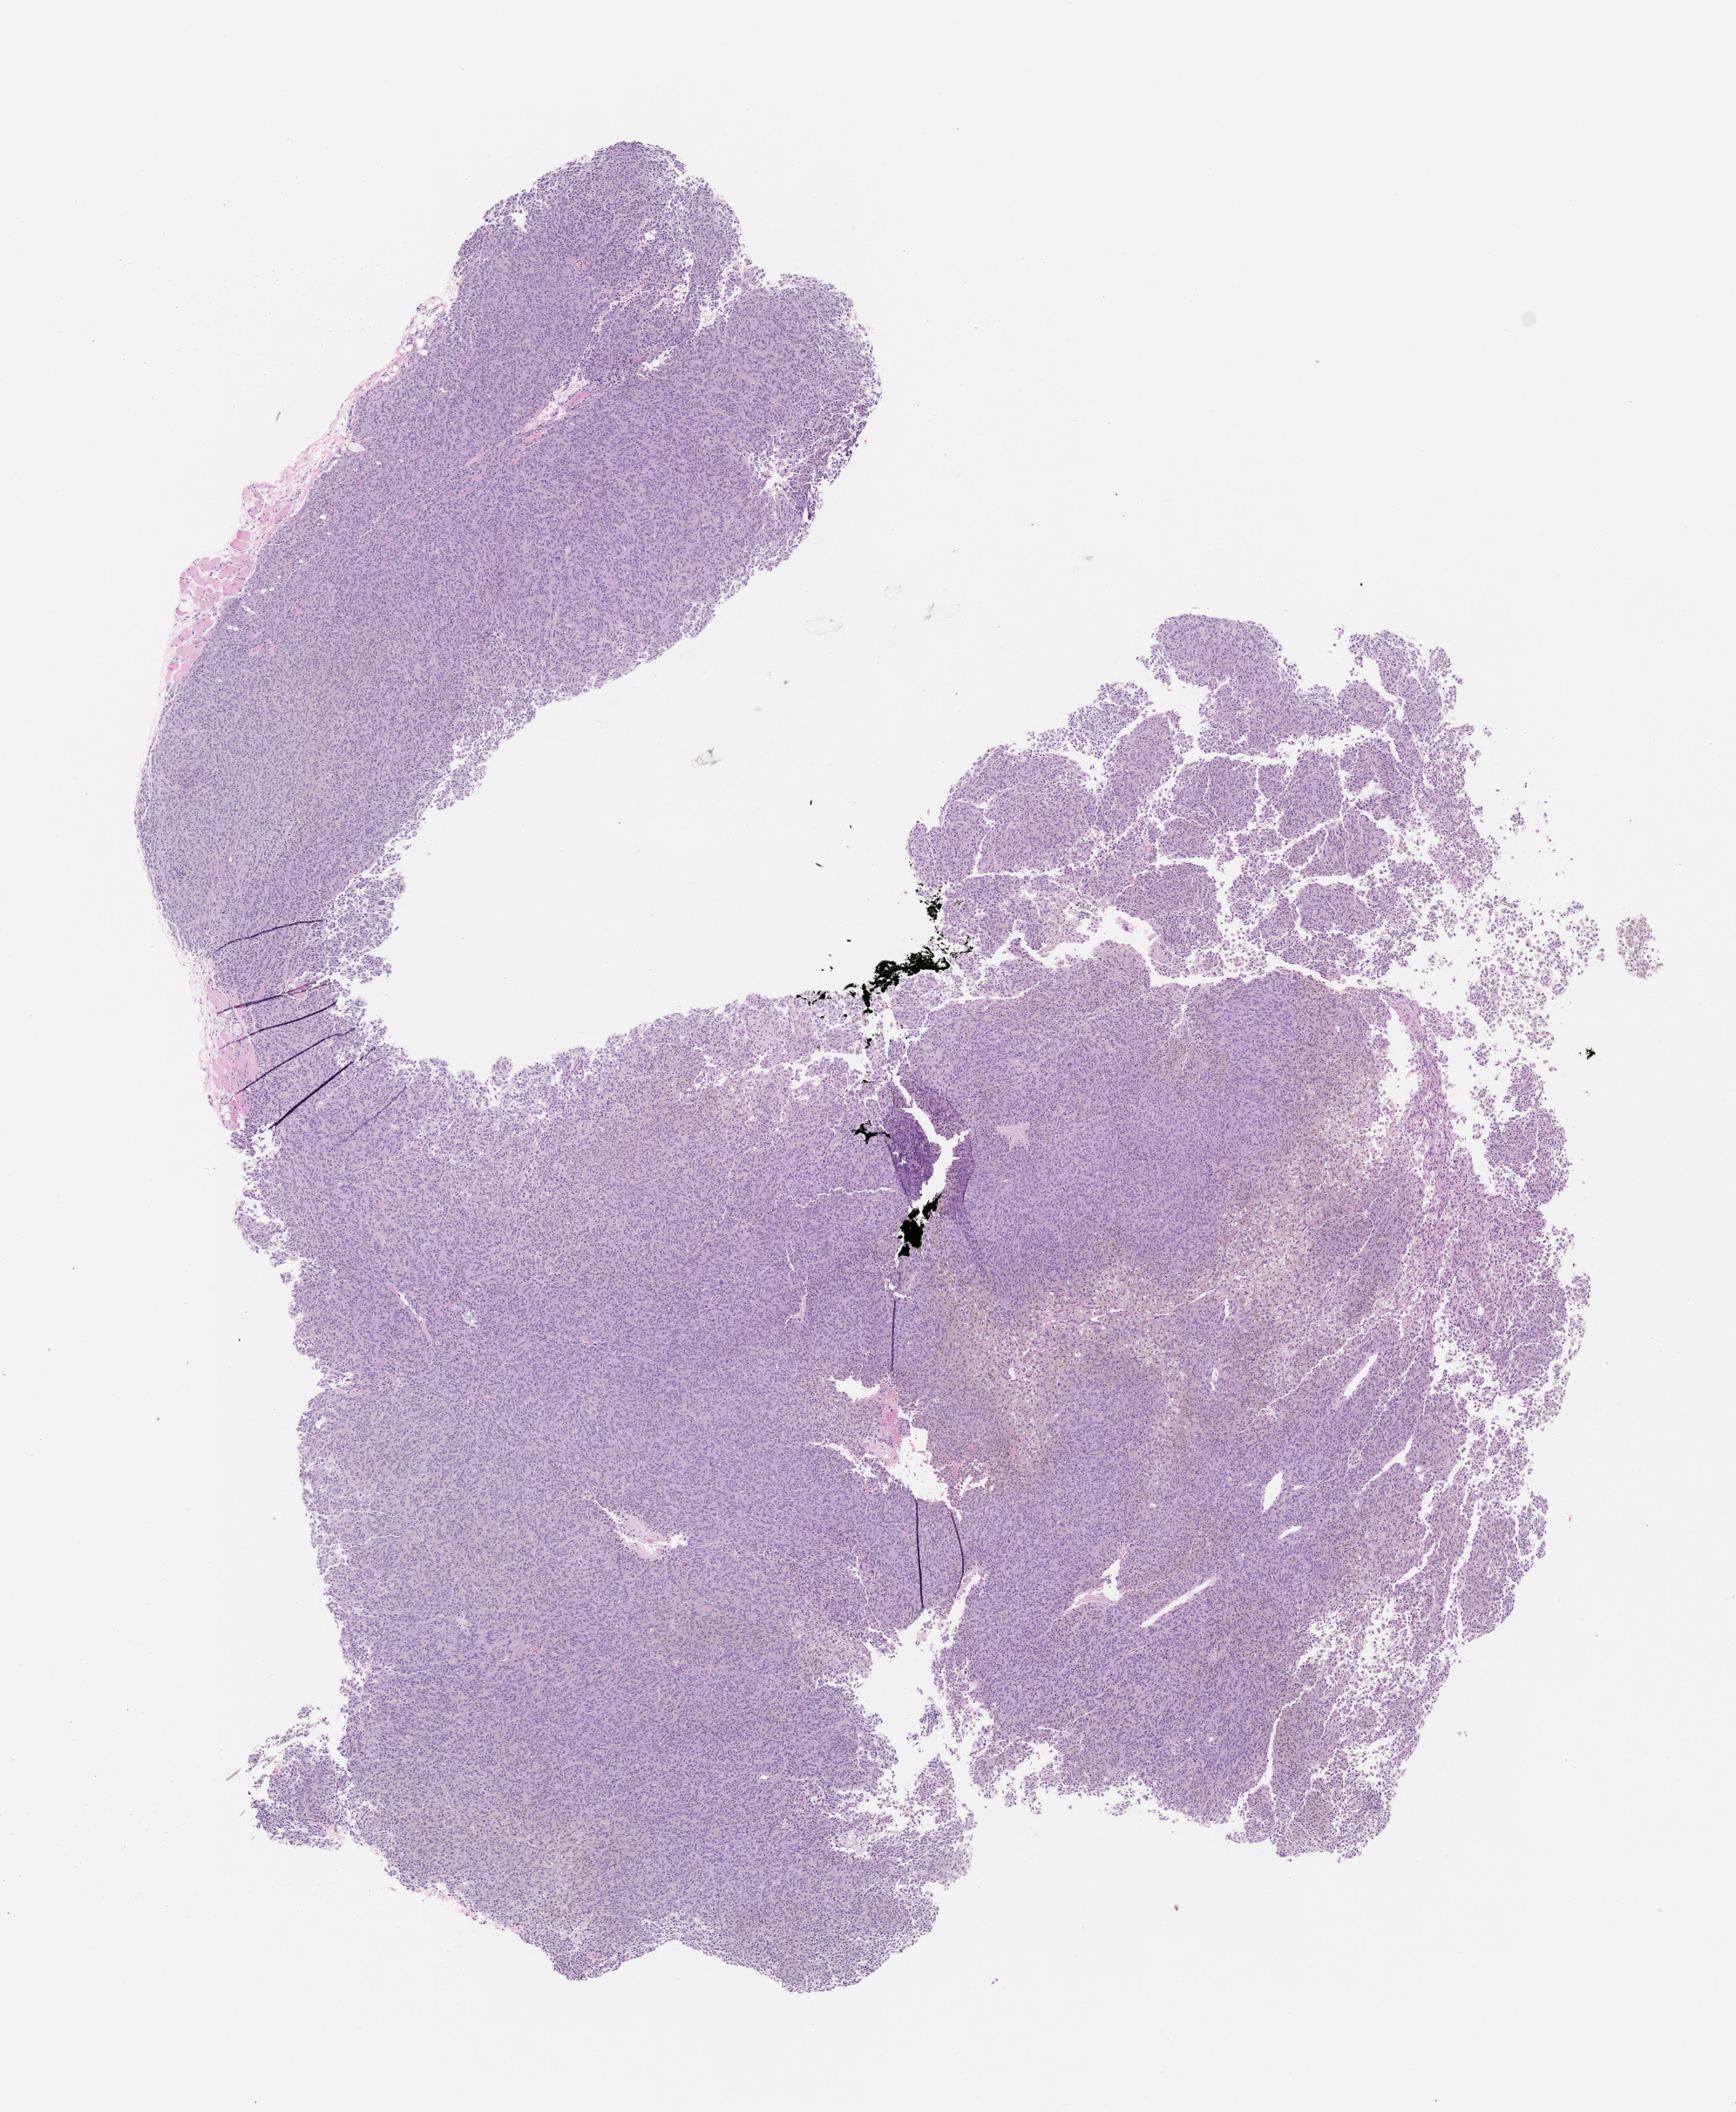
Whole-slide image, H&E: patient-derived xenograft (human tumor grown in a mouse), passage 1, whole scanned area (about 8.0 x 9.7 mm) shown as a low-resolution overview, FFPE section, originating tumor site category: skin.
Originating patient diagnosis: Melanoma.